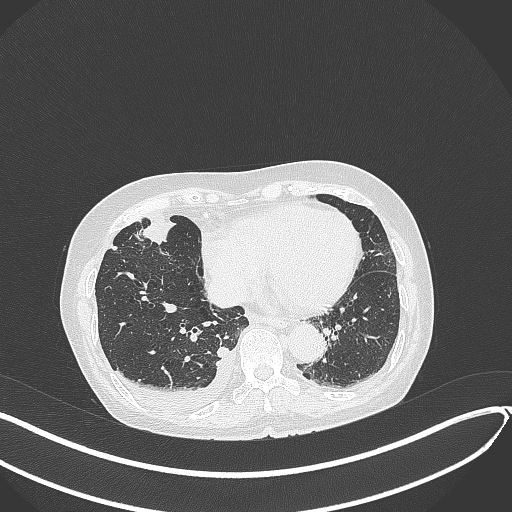
Chest CT, one axial slice; position 122 of 418 along the scan axis; 120 kVp; lung window (W 1500 / L -600 HU); 1 mm slice thickness; 512 × 512 image matrix, field of view 400 × 400 mm. Female patient, age 75 years. From the clinical record (not read from this slice): clinical TNM (as recorded): T2a N3 M0.
Structures marked on this image (rectangle marked by the reading radiologist):
- lung tumour (recorded histology: adenocarcinoma): bounding box <138,214,175,244> (left, top, right, bottom; pixels)